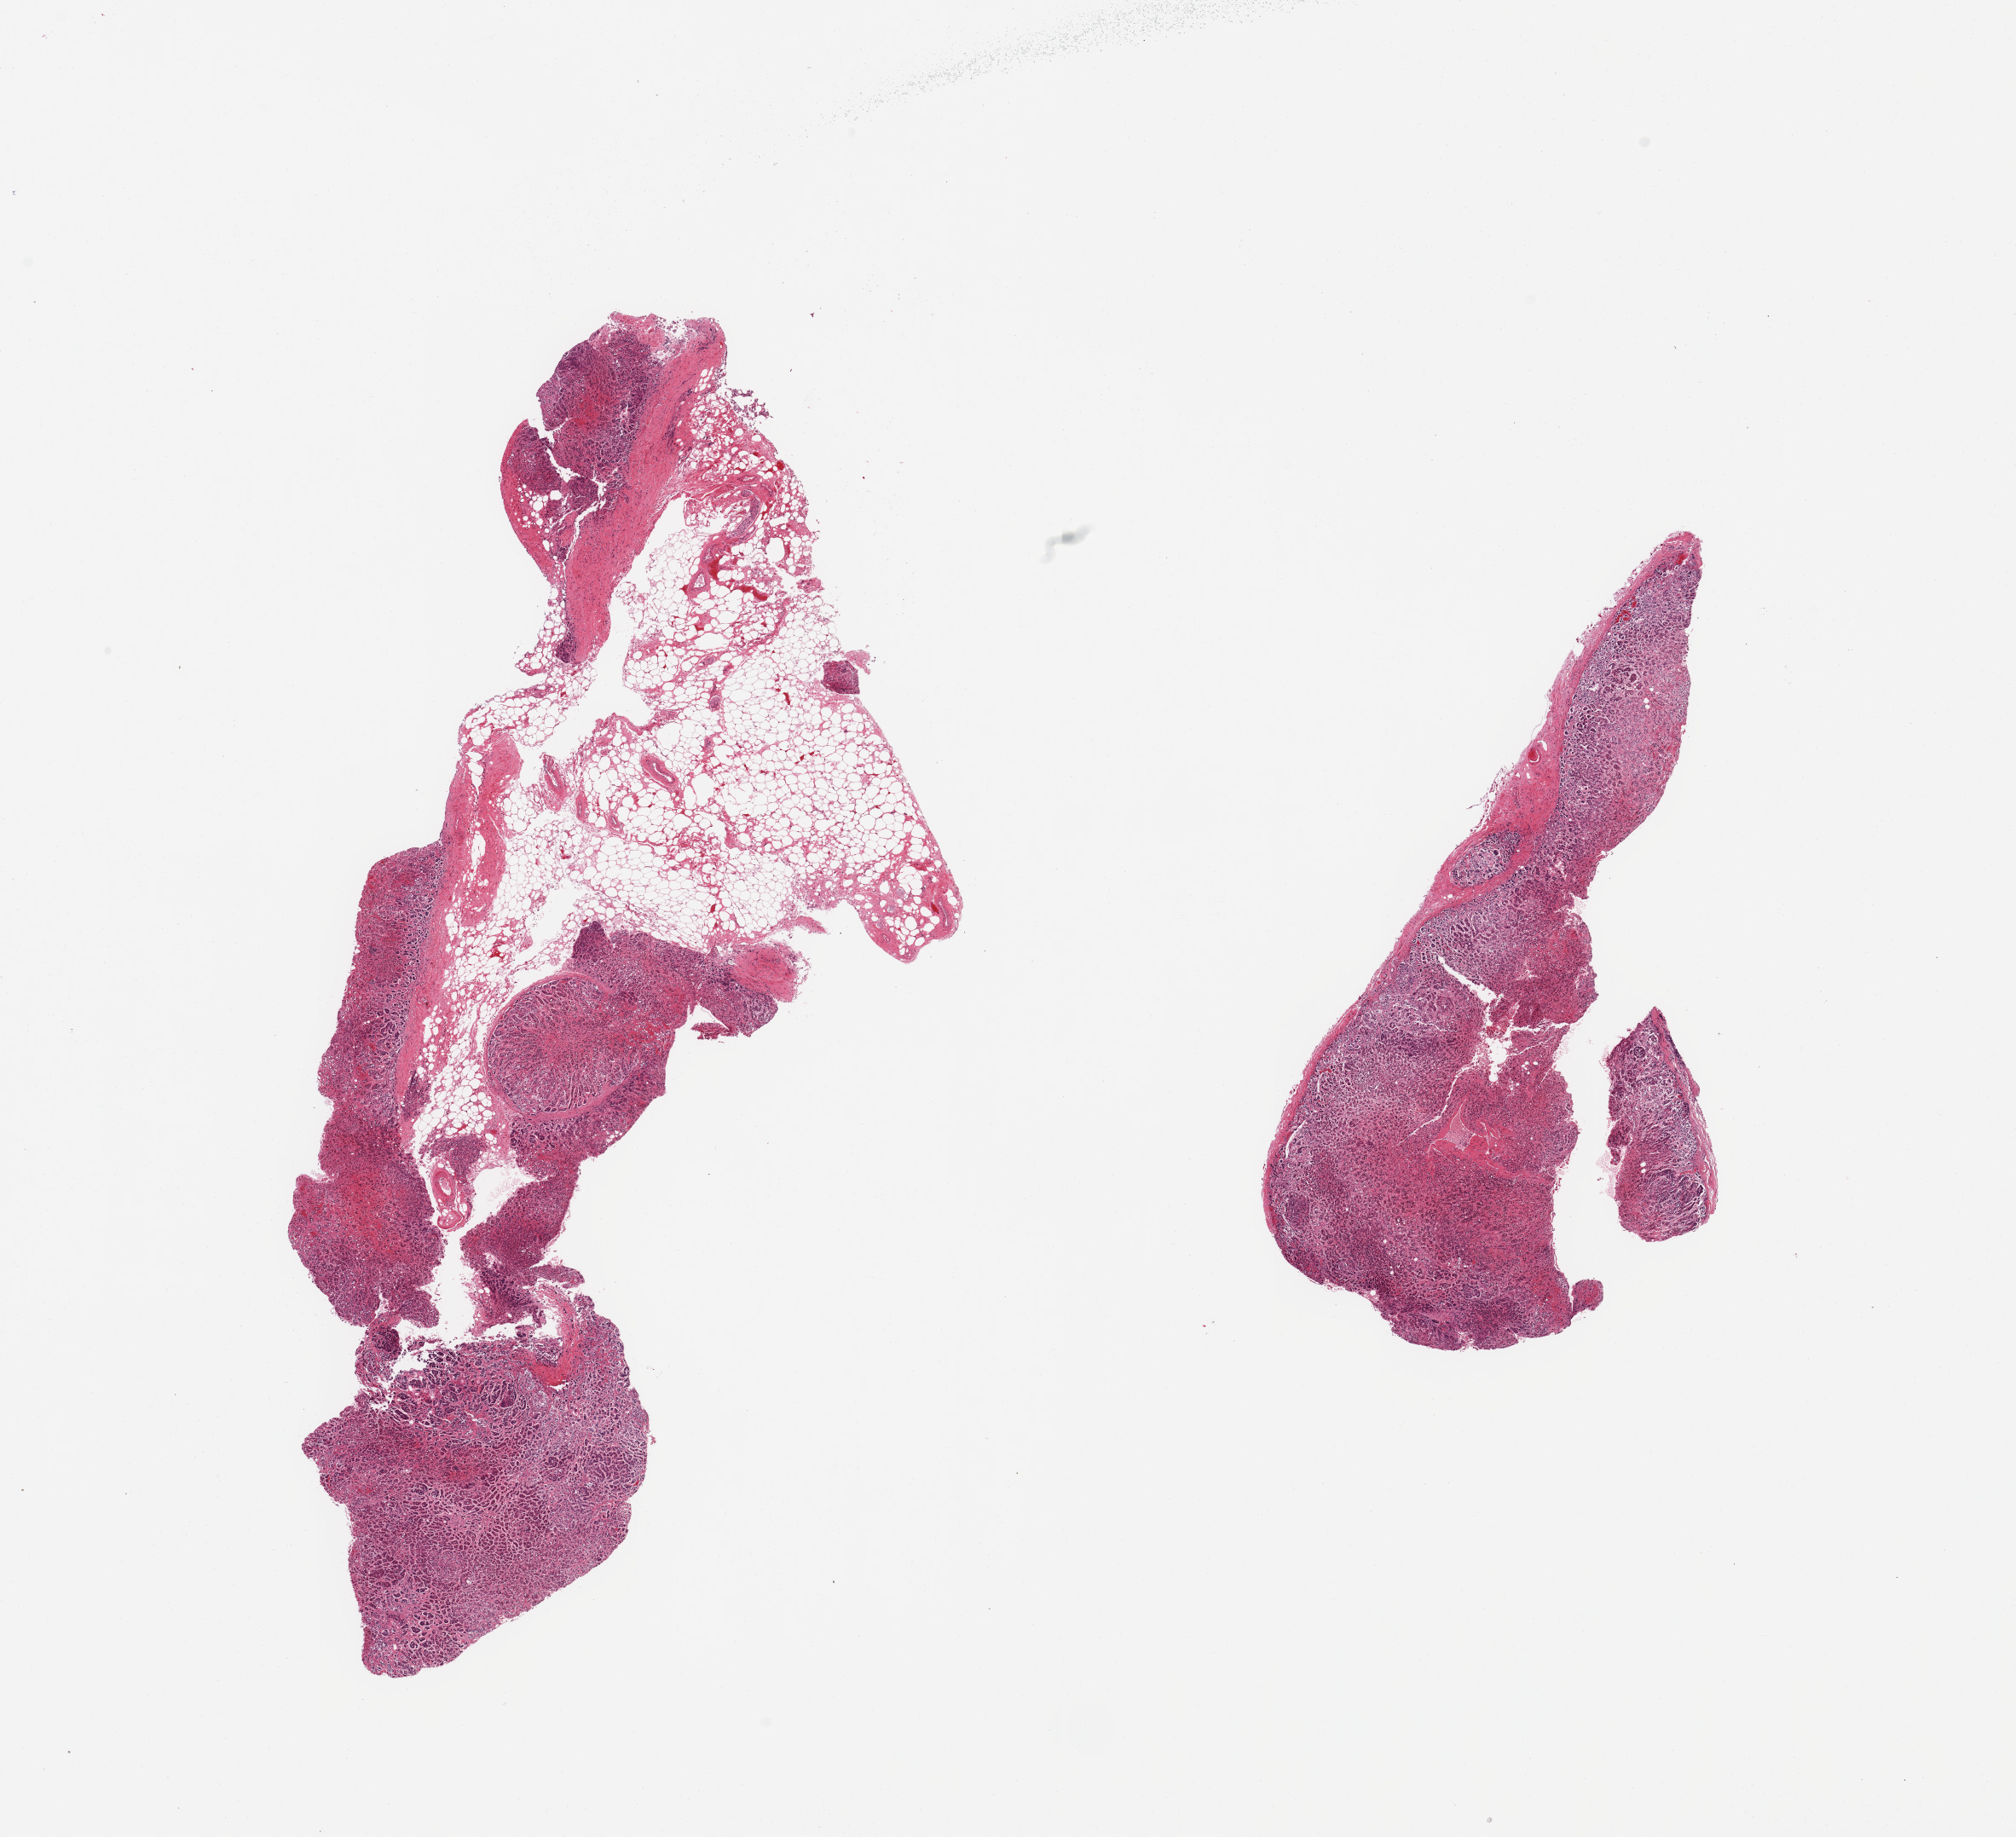
Whole-slide image, haematoxylin and eosin stain, a low-resolution overview of the entire scanned area, about 18.7 x 17.0 mm (slide scanned at 20x), PAXgene-fixed, paraffin-embedded tissue, section of adrenal gland (target tissue), donor tissue sample.
Reviewer comment on this tissue sample: 2 pieces; 1 with 50% internal & external fat.